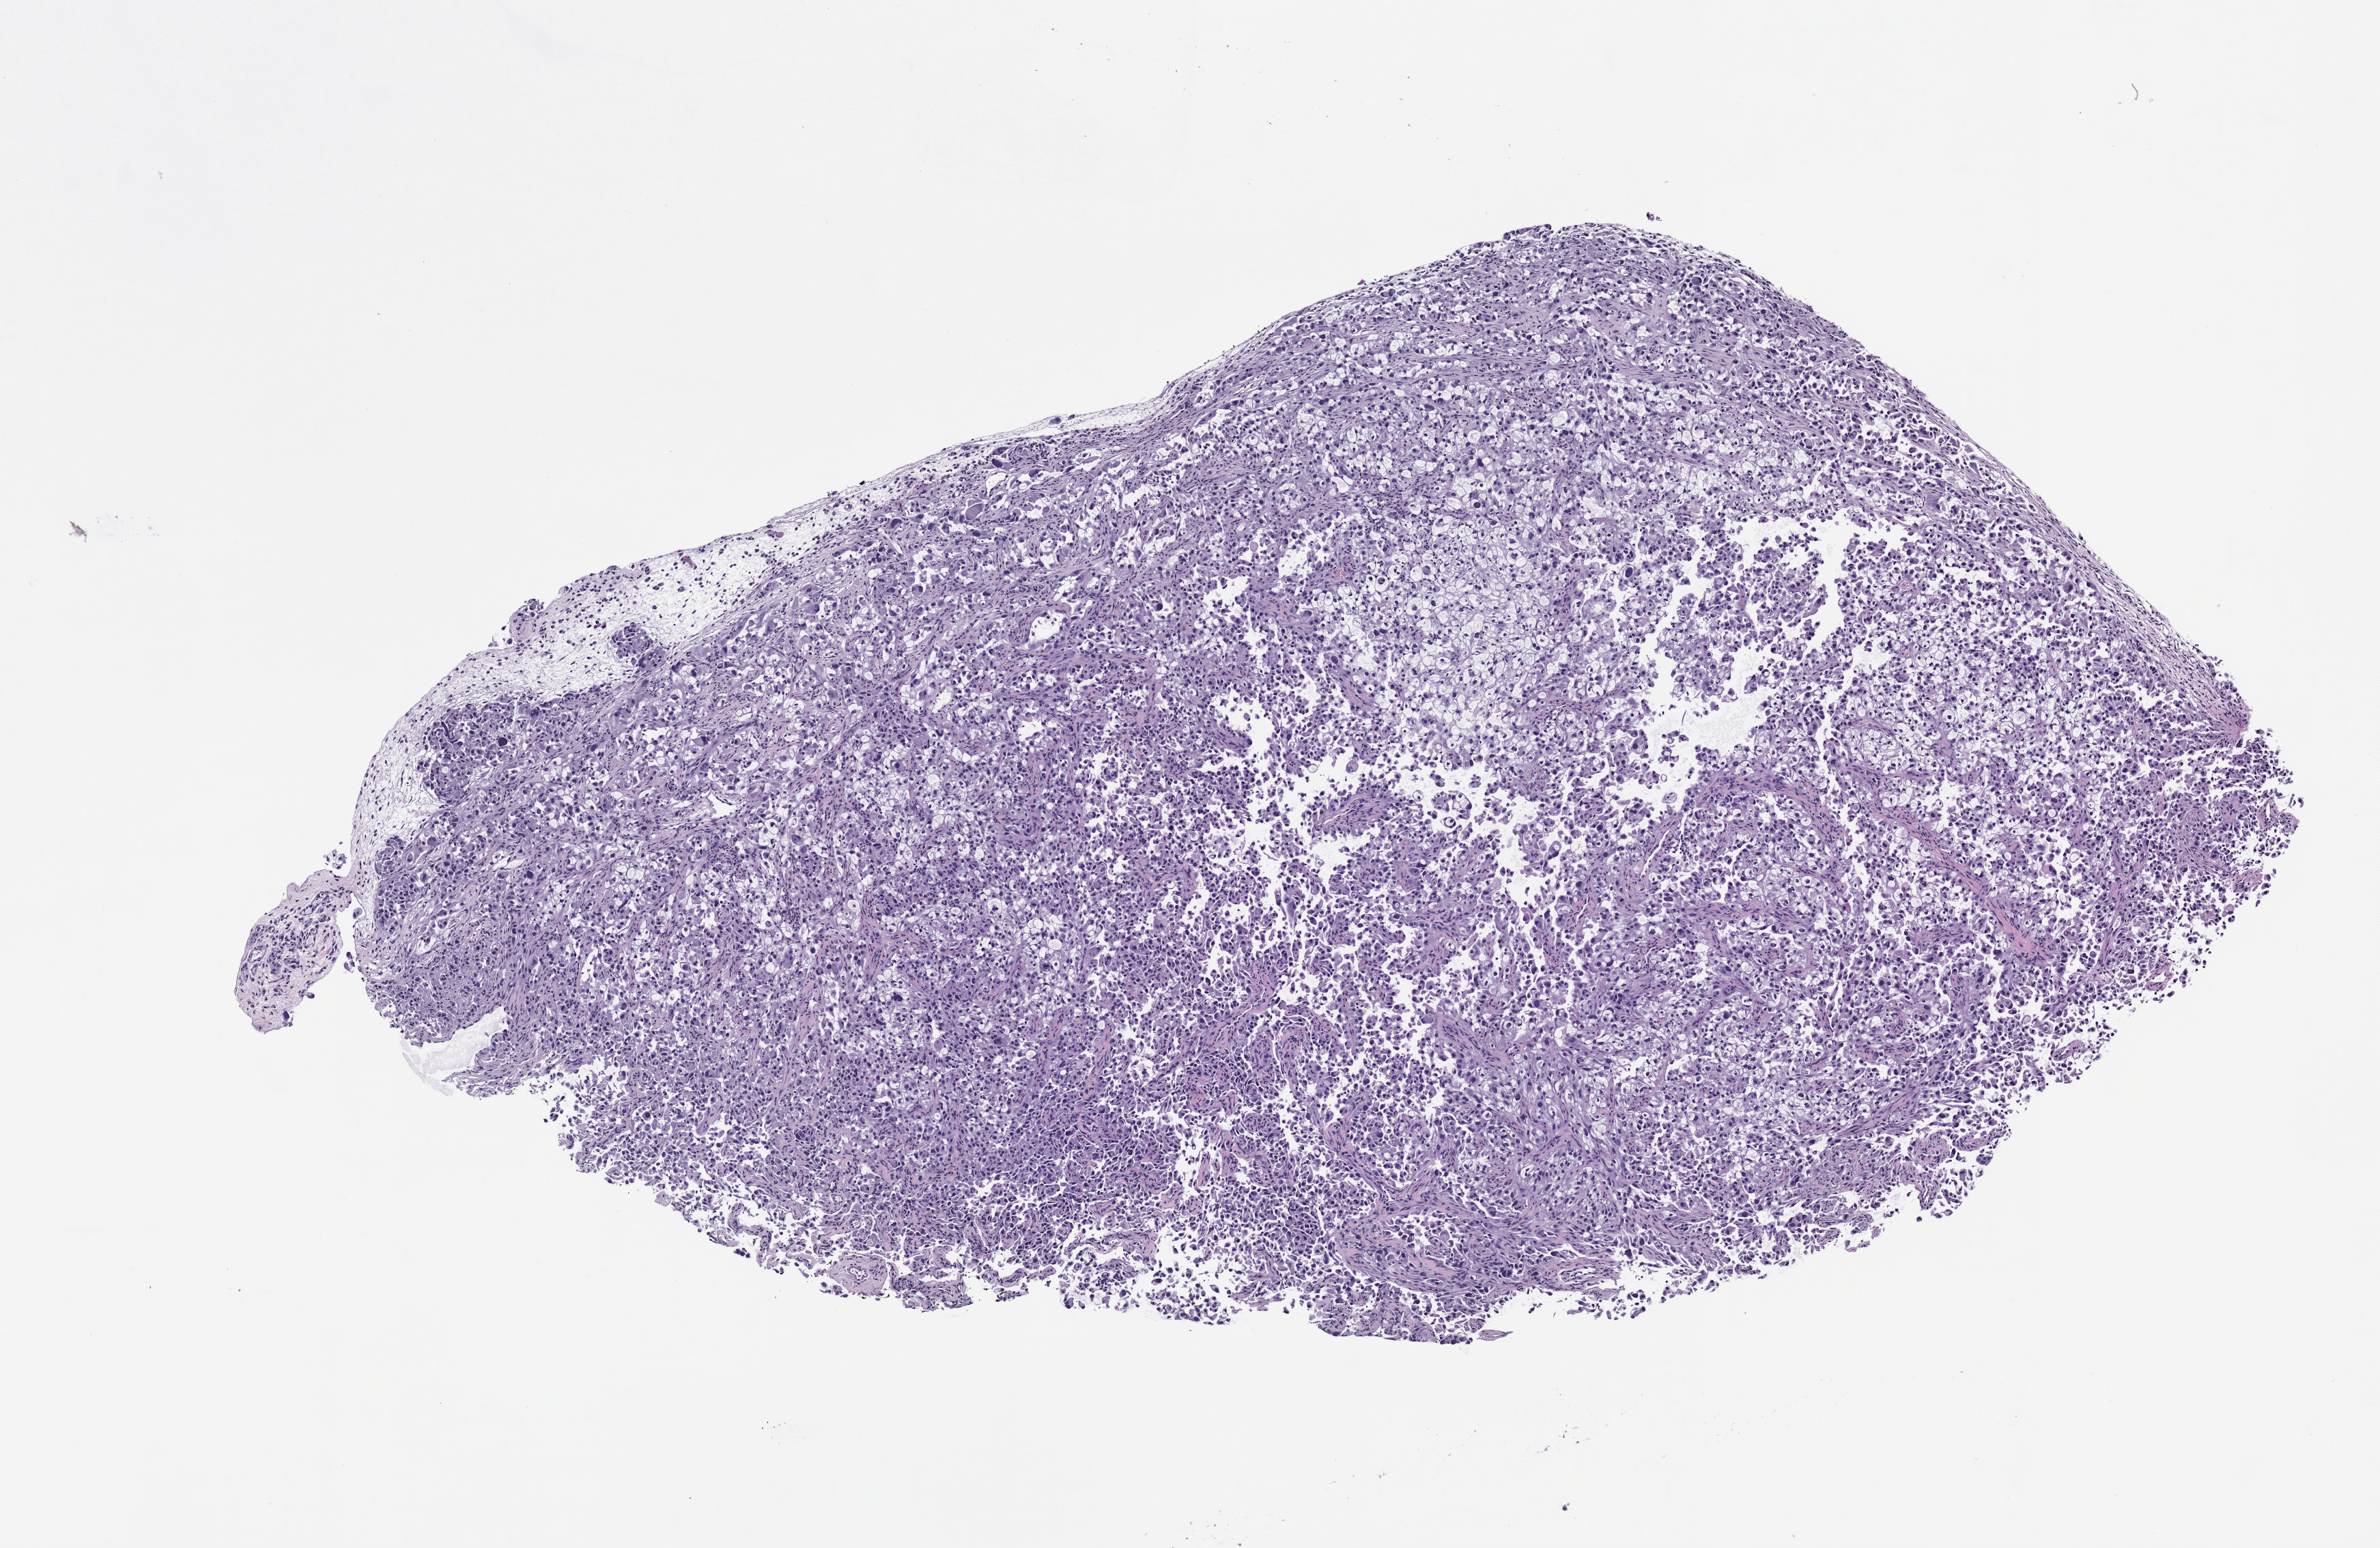
Whole-slide image, hematoxylin and eosin (H&E): patient-derived xenograft (human tumor grown in a mouse), passage 2, a low-resolution overview of the entire scanned area, about 7.0 x 4.6 mm; FFPE section; tumor site category: genitourinary tract.
Originating patient diagnosis: Renal Cell Carcinoma, Not Otherwise Specified.